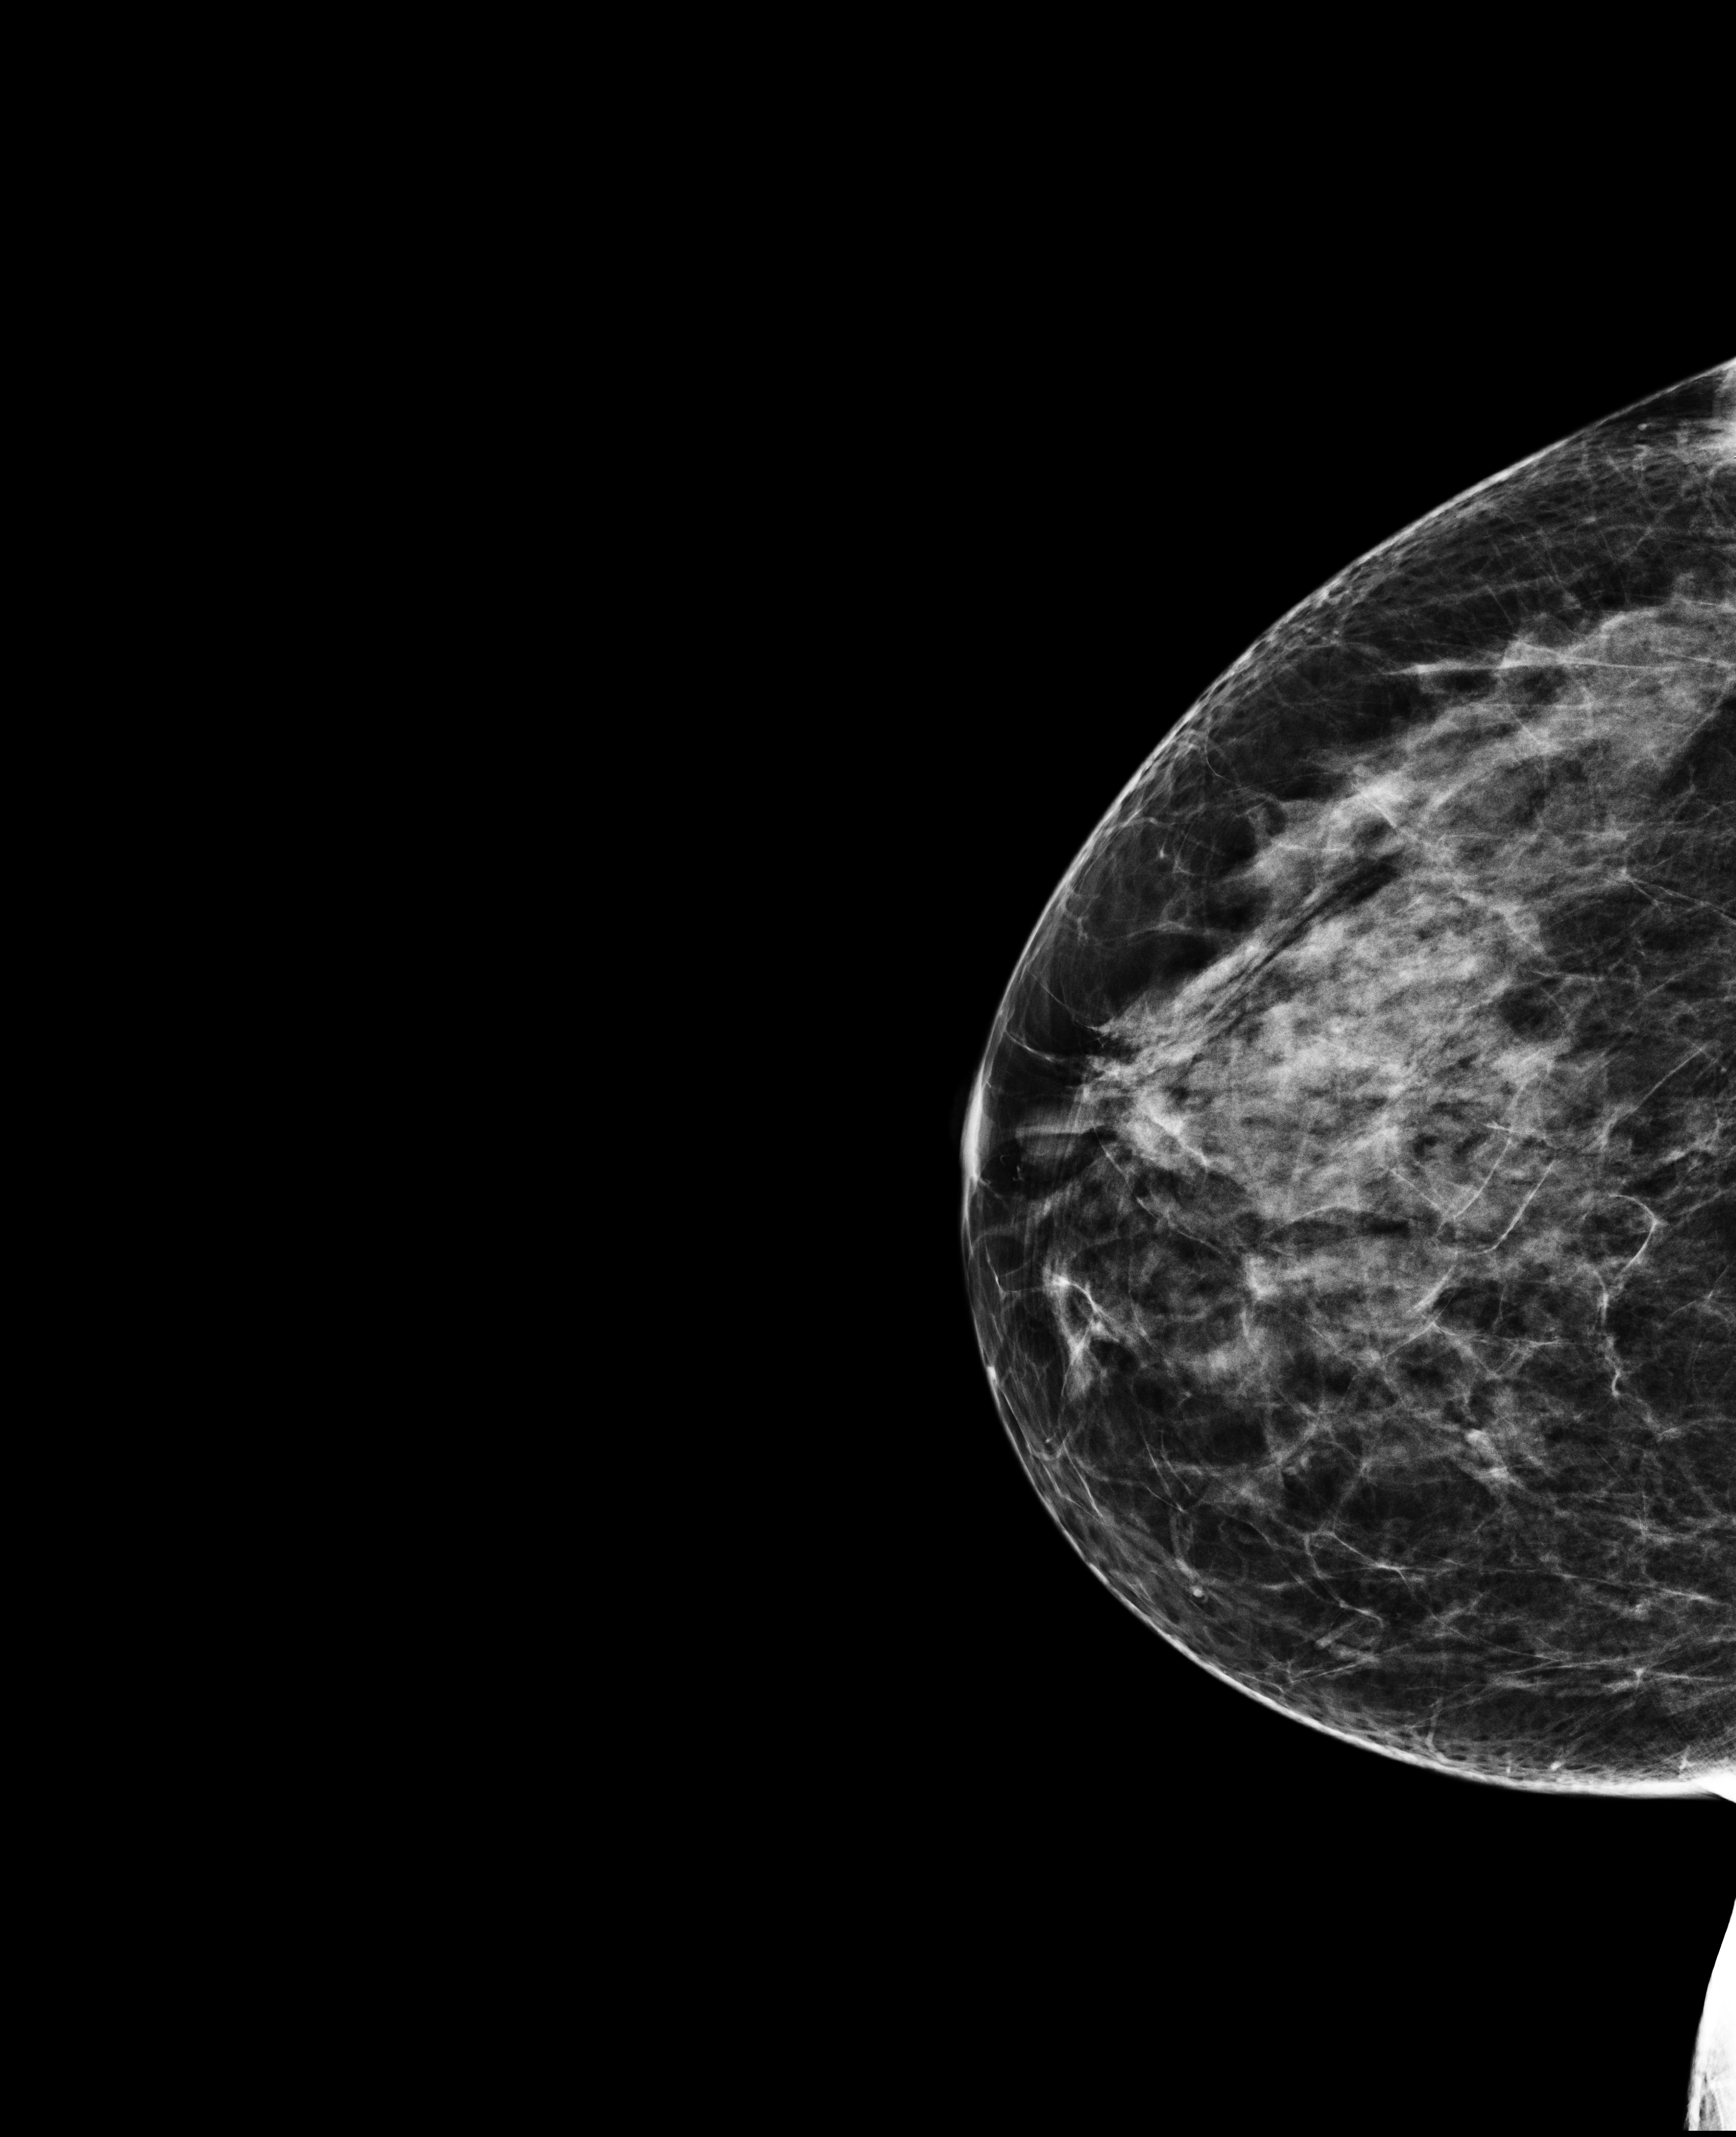
Annual screening mammography examination; compressed breast thickness 54 mm. Patient aged 48 years (female).
Image type: full-field digital mammogram. Breast: left. Projection: craniocaudal (CC) view.